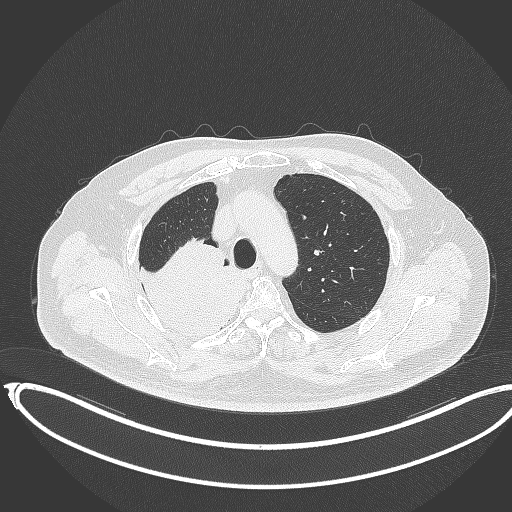
Chest CT, one axial slice. Position 280 of 403 along the scan axis. Lung window (W 1500 / L -600 HU). 1 mm slice thickness. 512 × 512 image matrix, field of view 436 × 436 mm. Male patient, age 68 years. From the clinical record (not read from this slice): clinical TNM (as recorded): T2a N0 M0.
Outlined on this slice (rectangle marked by the reading radiologist):
- lung tumour (recorded histology: adenocarcinoma): bounding box [x1, y1, x2, y2] px = [131, 238, 248, 340]